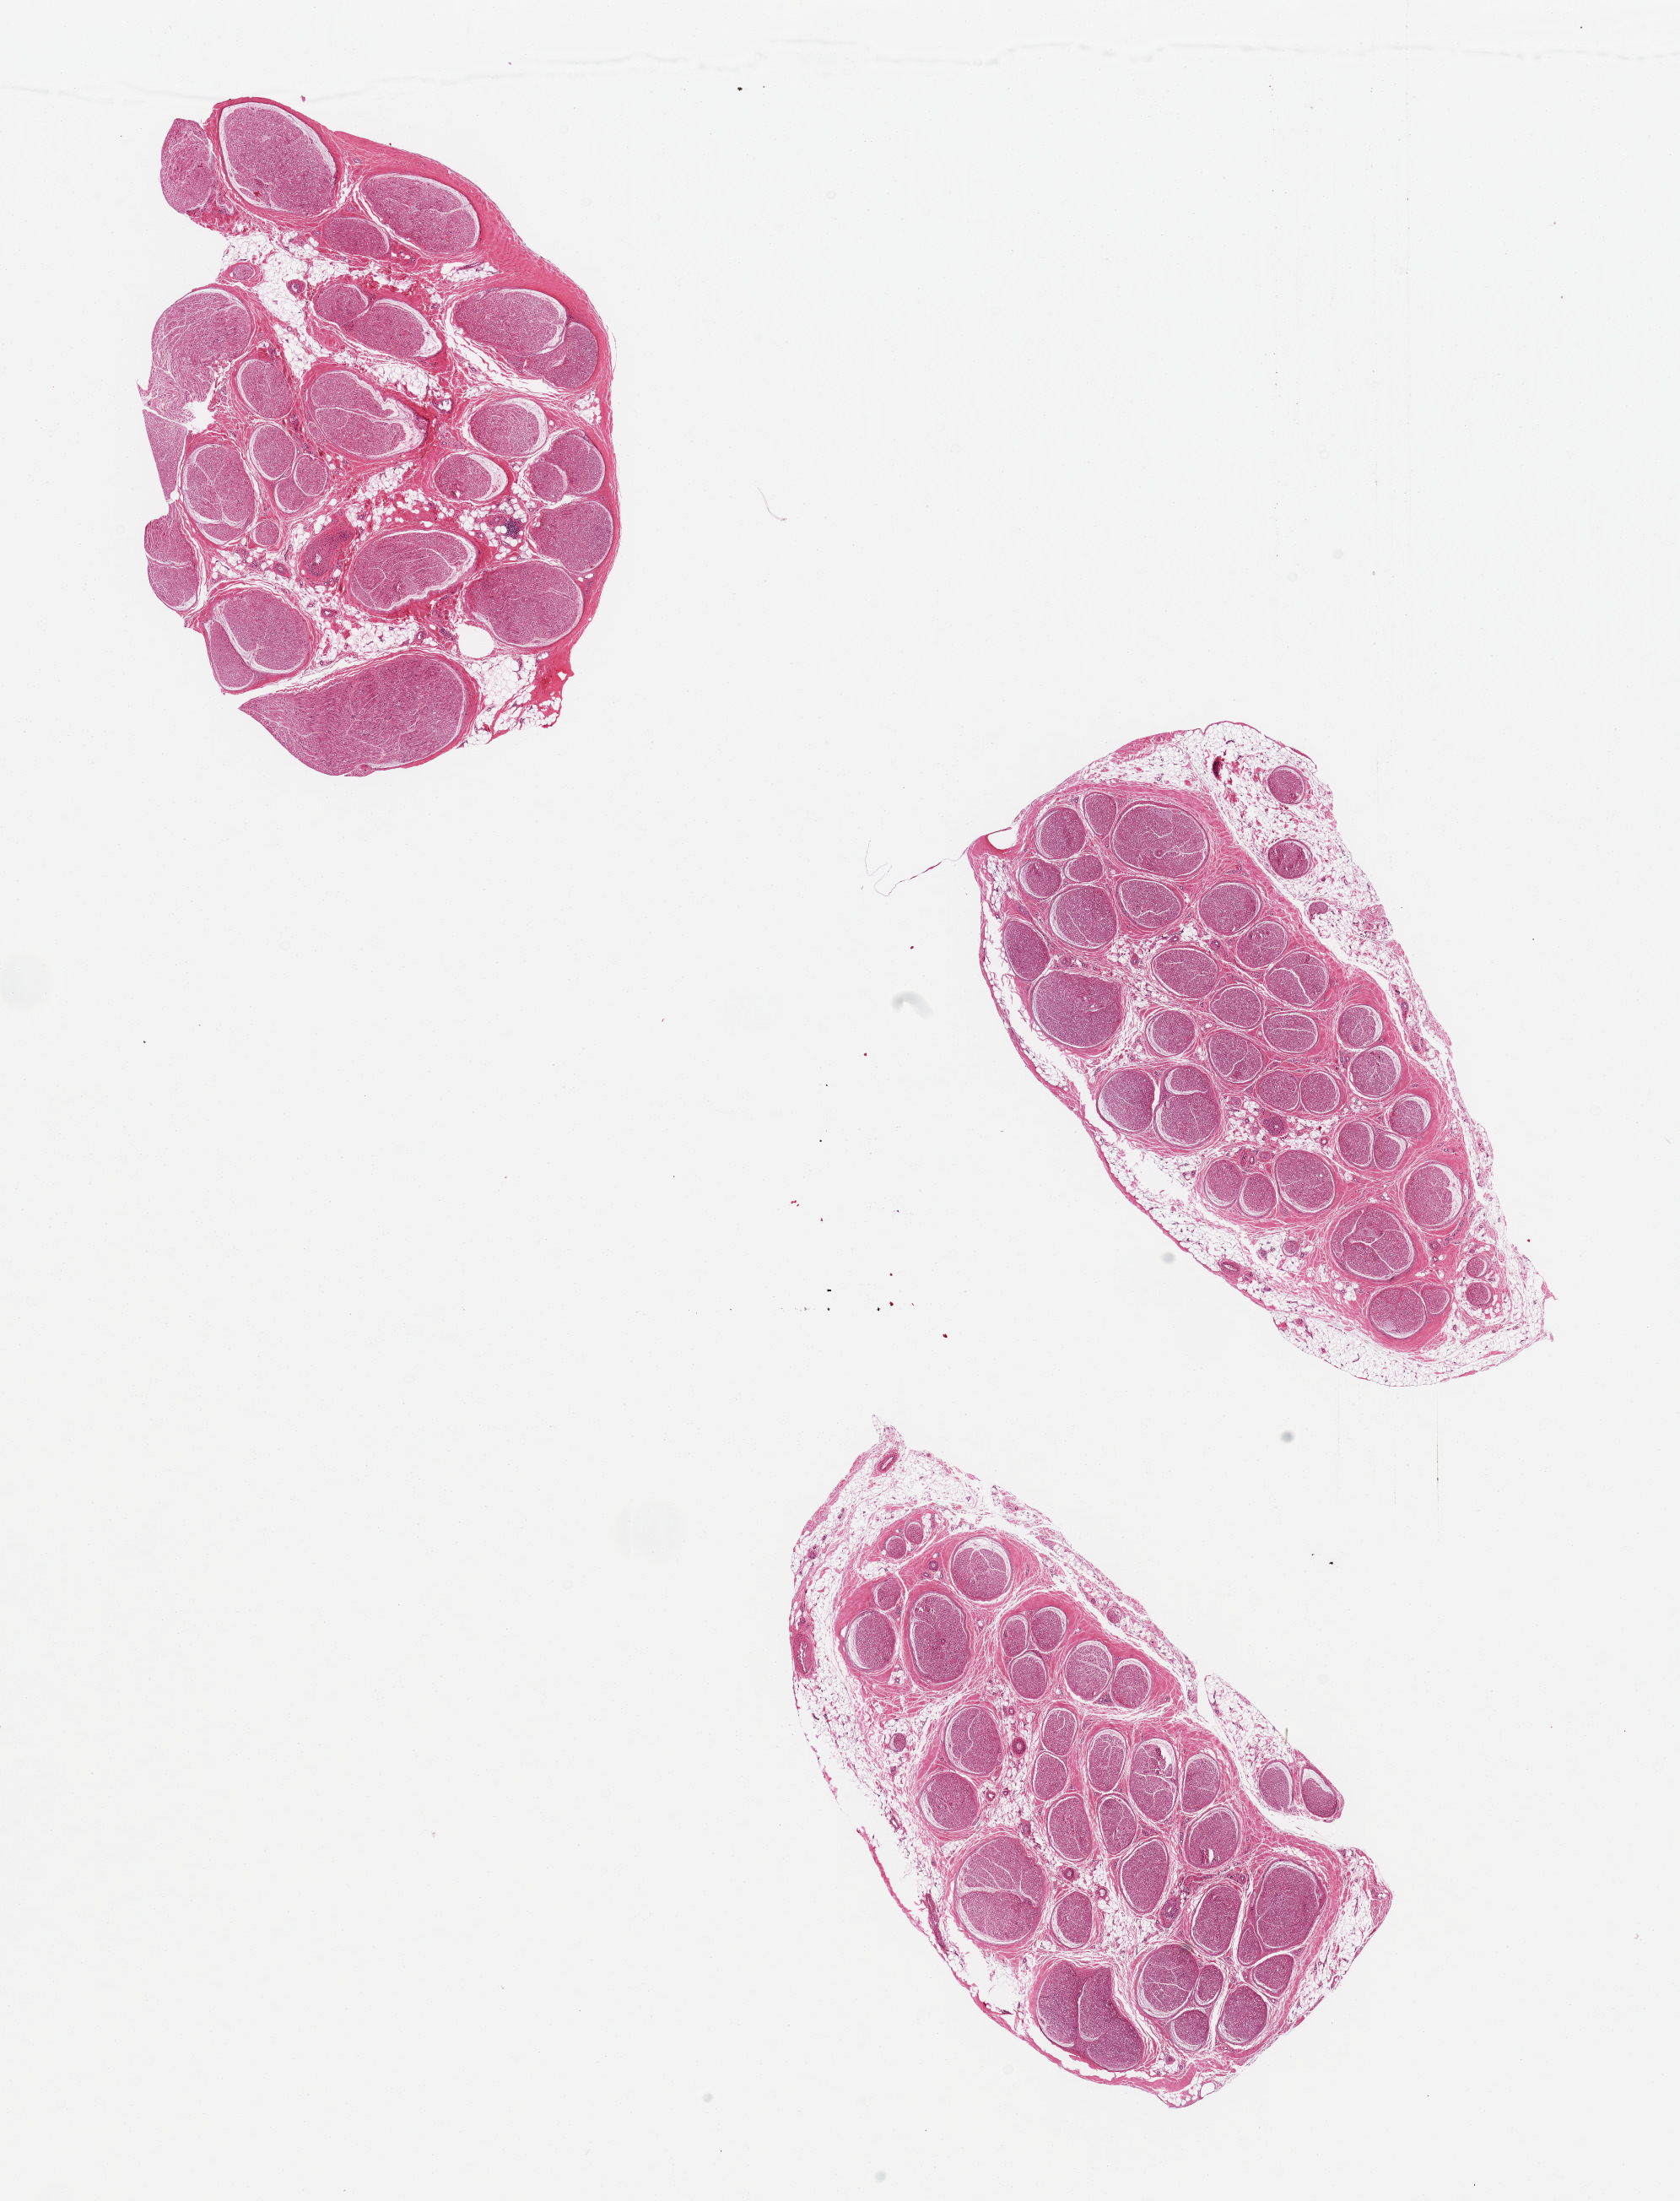
Digitized haematoxylin and eosin-stained section — shown as a low-resolution overview of the whole scanned area (about 15.8 x 20.6 mm); PAXgene-fixed, paraffin-embedded tissue; section of tibial nerve (target tissue); donor tissue sample. Donor sex: male.
Reviewer comment on this tissue sample: 3 pieces, discontinuous rims of adherent fat up to ~0.5mm.